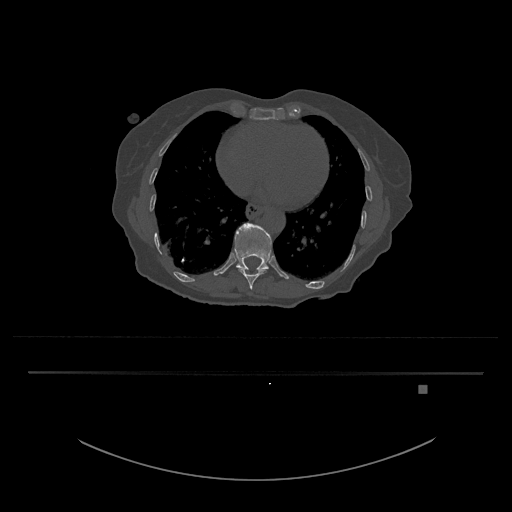
CT including the spine, one axial slice; slice 690 of 797 in the series (ordered by position); reconstruction kernel Br40s/3; 120 kVp; bone window (W 1800 / L 400 HU); 0.5 mm slice thickness; 512 × 512 image matrix. Female patient, age 57 years. Case-level facts recorded for this patient, not image findings: primary cancer: cervical.
Structures marked on this image (semi-automatic segmentation, software-assisted and operator-edited):
- T10 vertebra: bounding box [x1, y1, x2, y2] px = [239, 269, 267, 290]
- T11 vertebra: [234, 223, 272, 270]